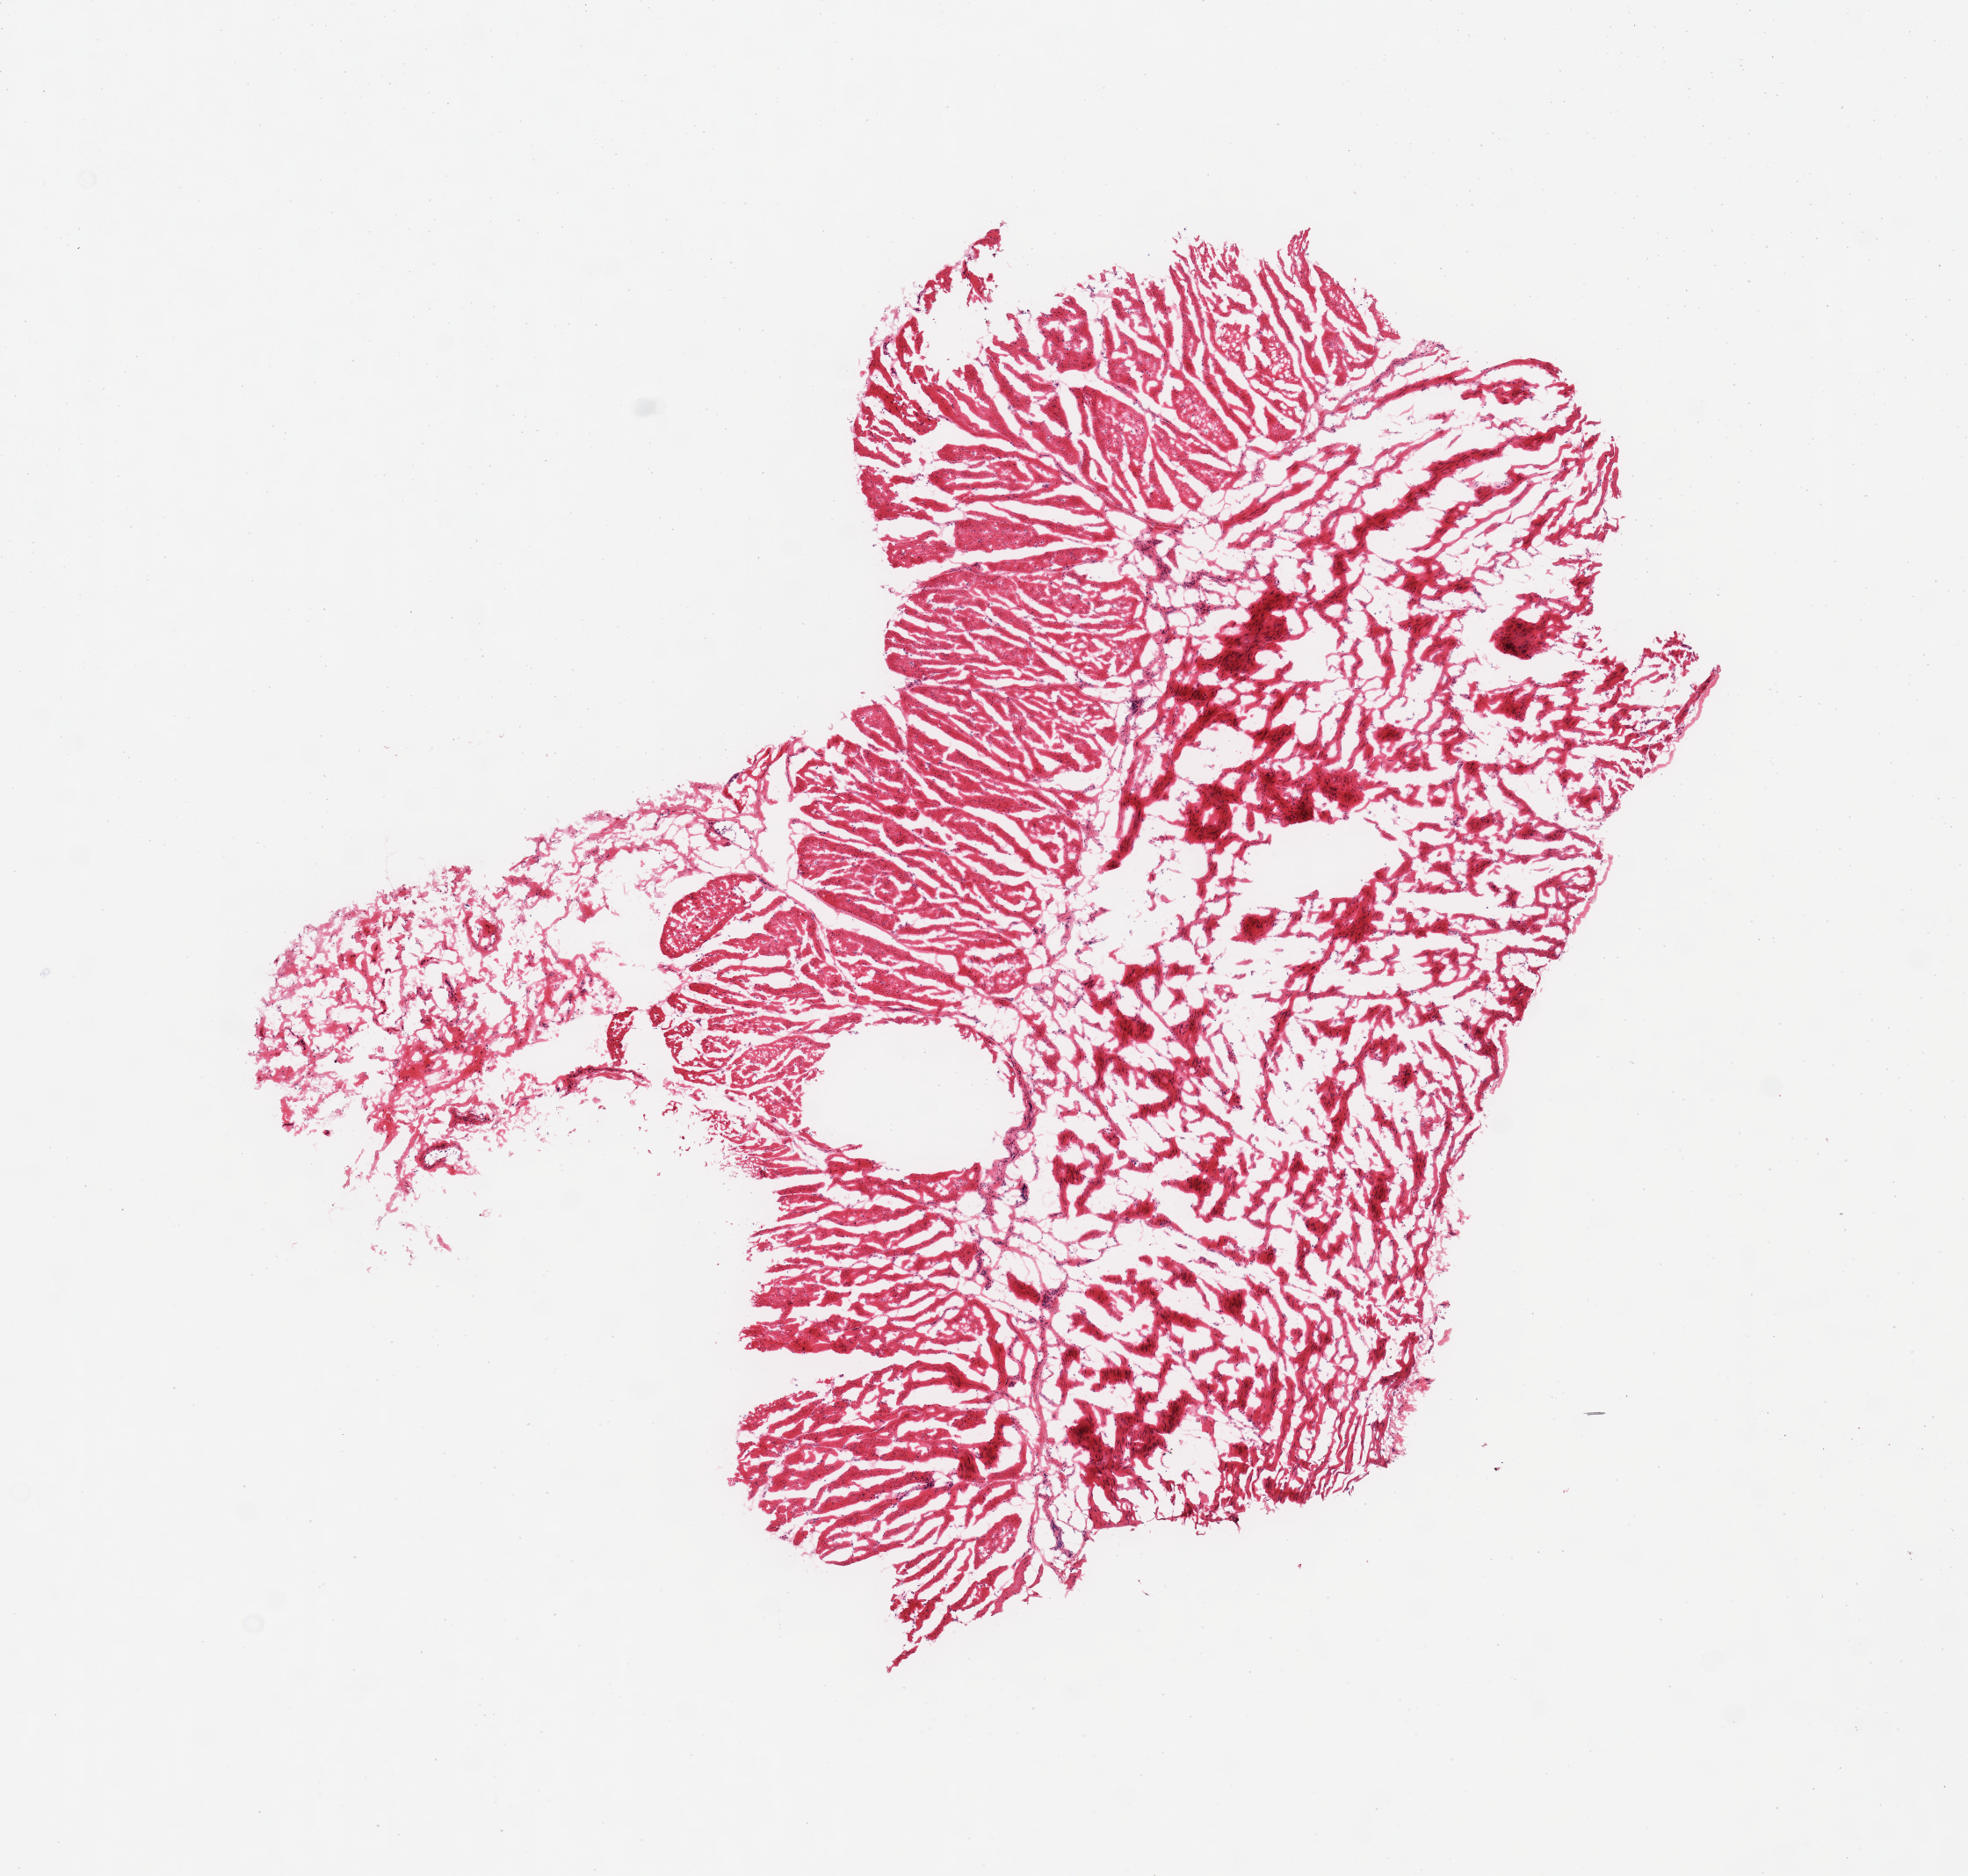
Whole-slide image, haematoxylin and eosin stain, whole scanned area (about 8.9 x 8.4 mm) shown as a low-resolution overview; frozen section; target tissue: esophageal muscle; tissue donor sample. Donor: male.
- review note (as recorded): 1 piece; comparable to PAXgene sample